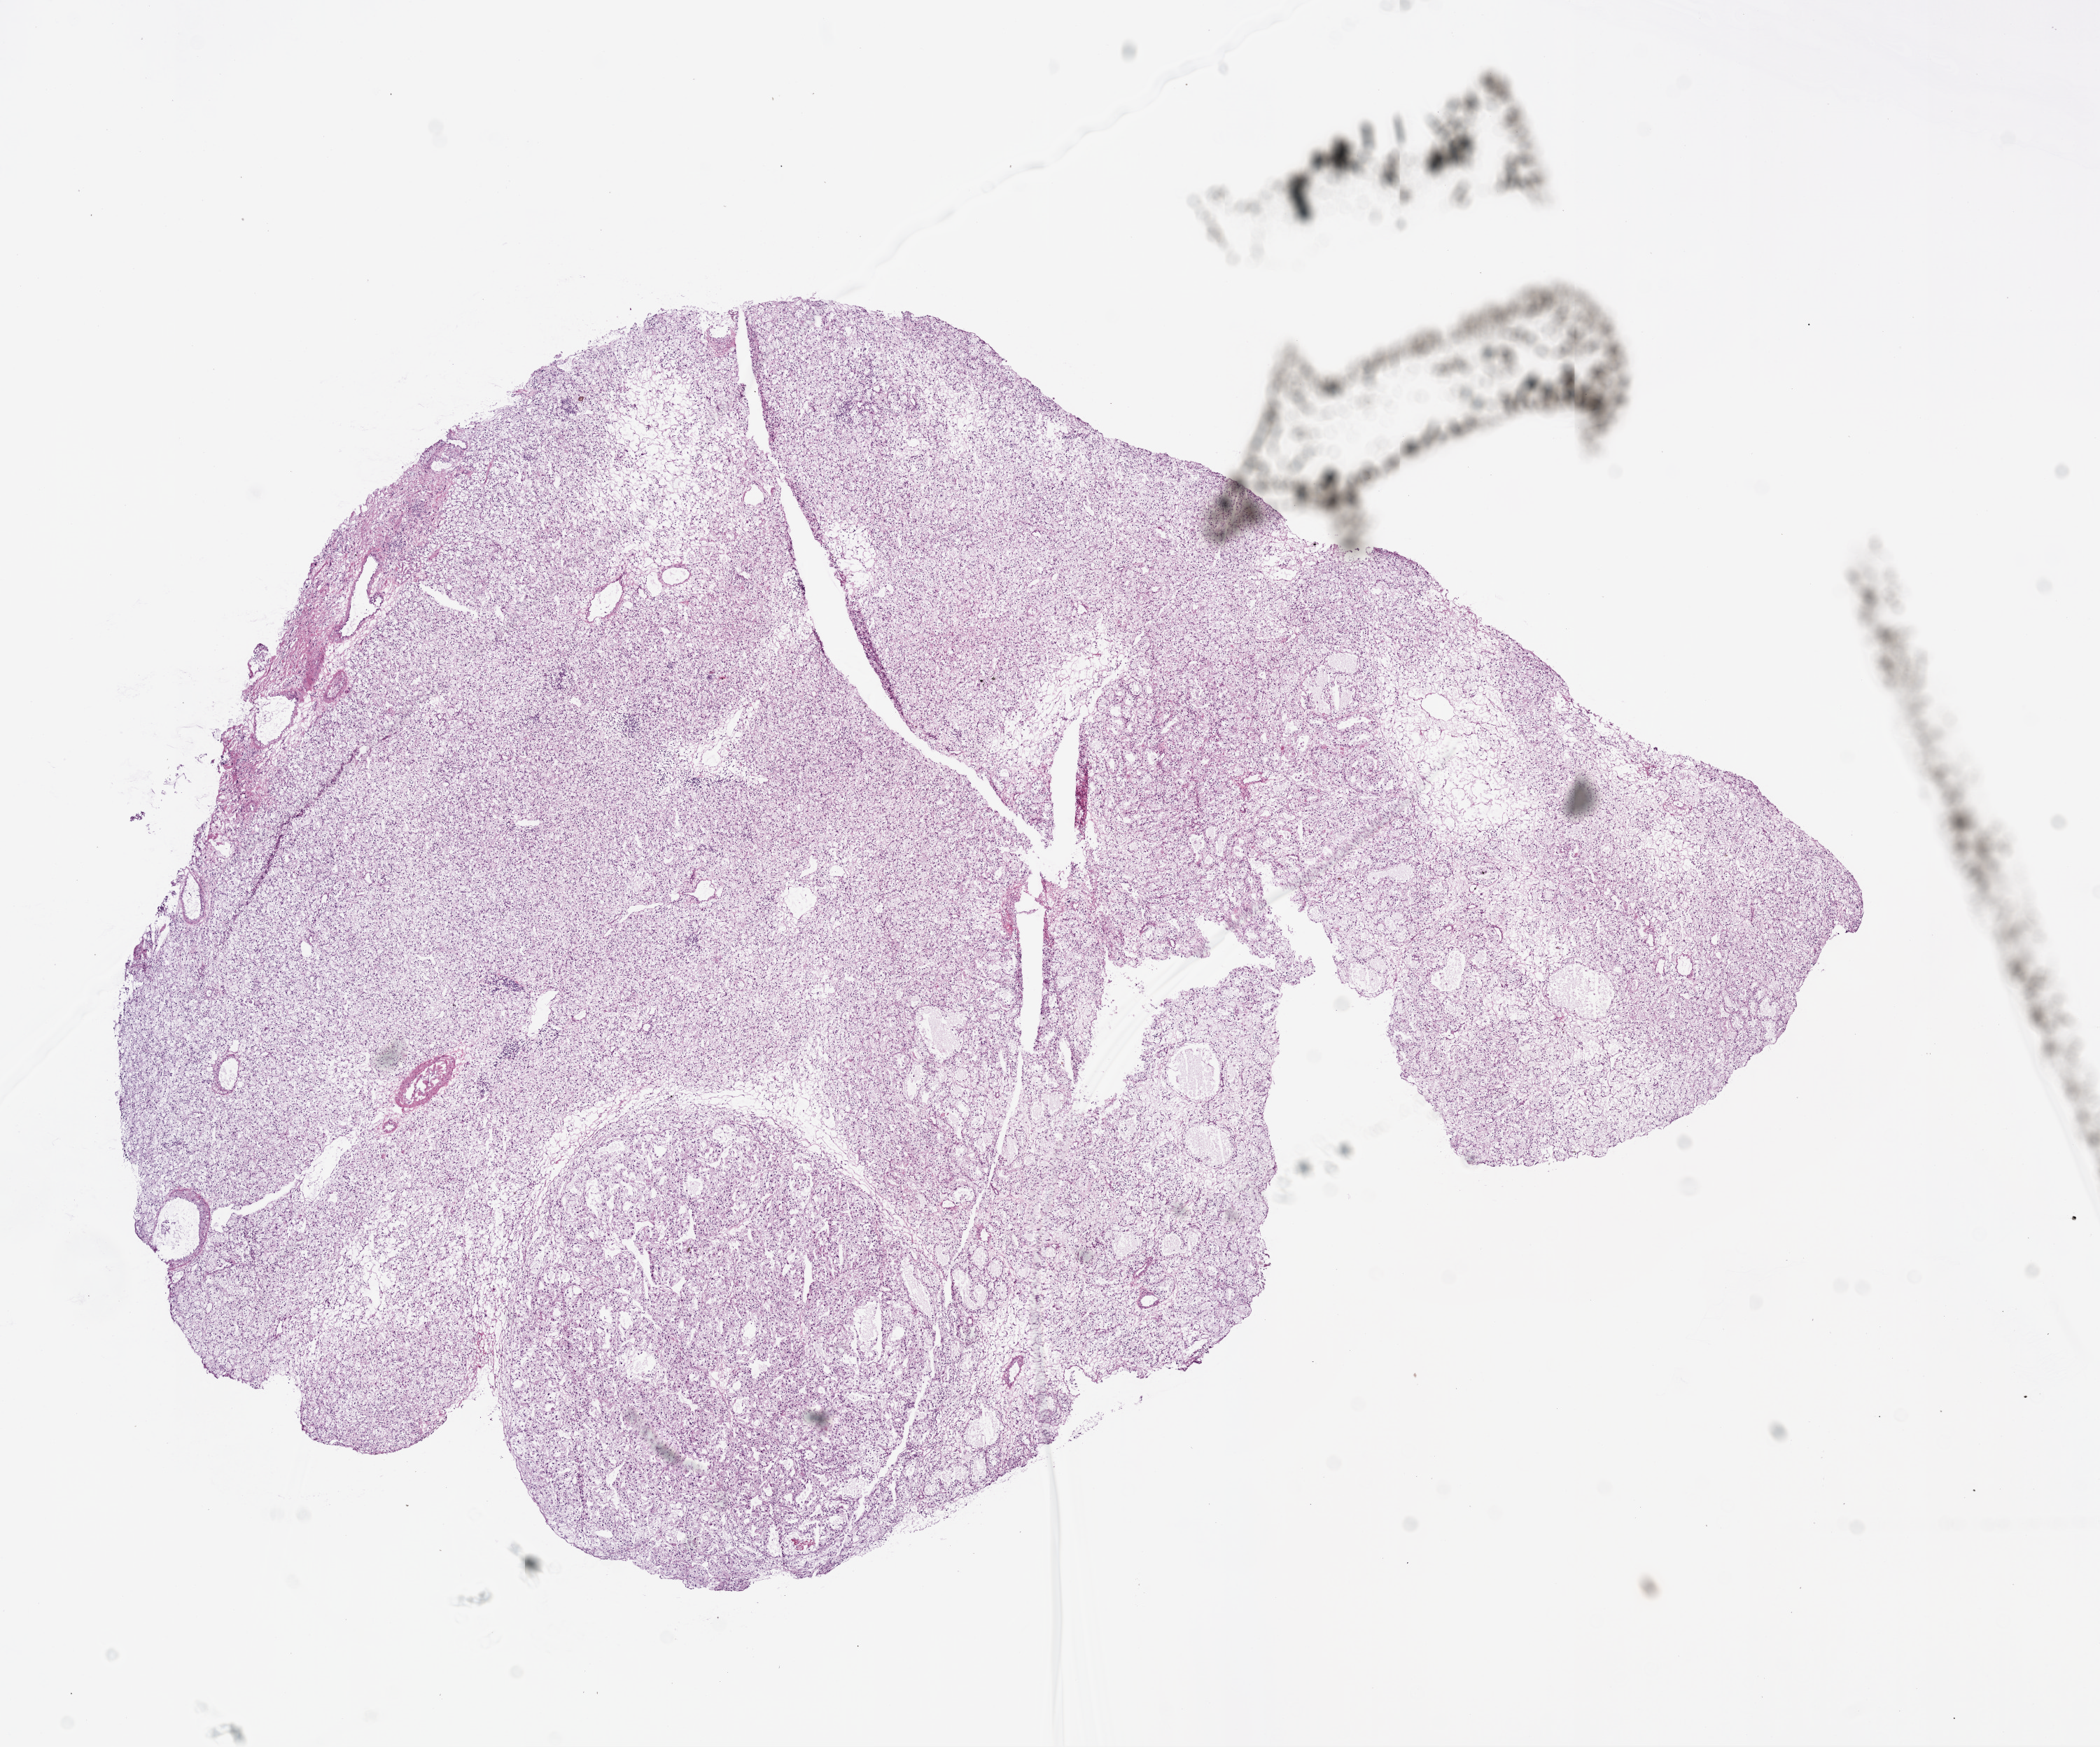
Digitized Hematoxylin and eosin (H&E) stained tissue section (whole slide) — a low-resolution overview of the entire scanned area, about 12.0 x 10.0 mm (acquisition: 20x scan); frozen section from the bottom of the tissue portion; primary tumour sample from the kidney. Patient: male, age at initial diagnosis 54 years. Histologic grade: G3 (poorly differentiated). Slide review estimates, as recorded: tumour cells 90%, tumour nuclei 85%, normal cells 5%, stromal cells 5%, necrosis 0%.
Pathologic diagnosis: Clear cell adenocarcinoma, NOS. Laterality: left. AJCC pathologic stage: I.